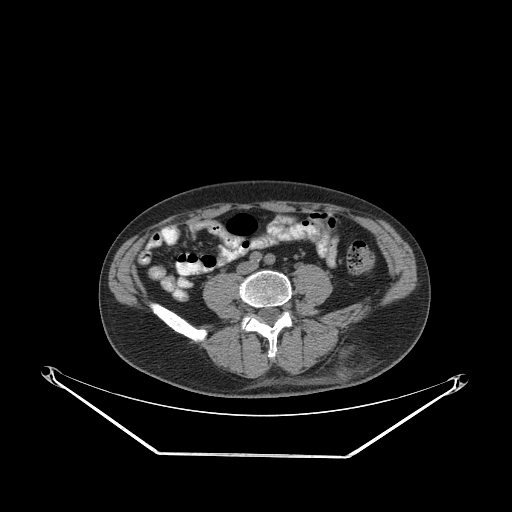
CT of an extremity soft-tissue mass (from a PET/CT study), one axial slice; position 94 of 267 along the scan axis; reconstruction kernel STANDARD; soft-tissue window (W 400 / L 40 HU); 3.75 mm slice thickness; 512 × 512 image matrix, field of view 500 × 500 mm. Male patient. From the clinical record (not read from this slice): histological type: leiomyosarcoma; grade: intermediate; site of the primary tumour: left pelvis.
Outlined on this slice (expert contour drawn on MRI and transferred to this co-registered scan by the dataset authors):
- gross tumour volume (mass): box from (x=329, y=343) to (x=360, y=375) px